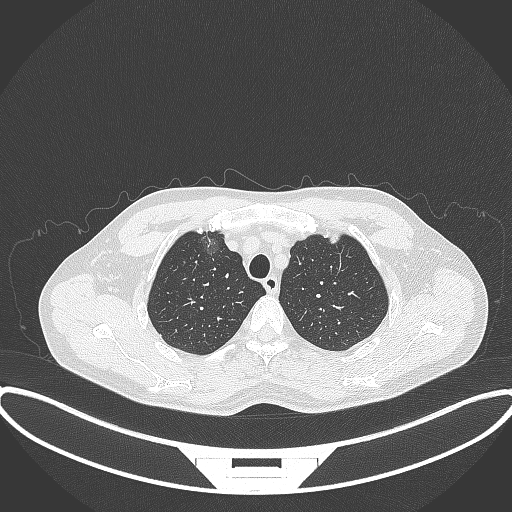
Chest CT, one axial slice. Slice 303 of 395 in the series (ordered by position). 120 kVp. Lung window (W 1500 / L -600 HU). 1 mm slice thickness. 512 × 512 image matrix, field of view 424 × 424 mm. Patient: male, 60 years. Case-level facts recorded for this patient, not image findings: clinical TNM (as recorded): T1c N0 M0.
Annotated regions visible in this slice (bounding box drawn by a radiologist):
- lung tumour (recorded histology: adenocarcinoma): bounding box <196,224,222,263> (left, top, right, bottom; pixels)